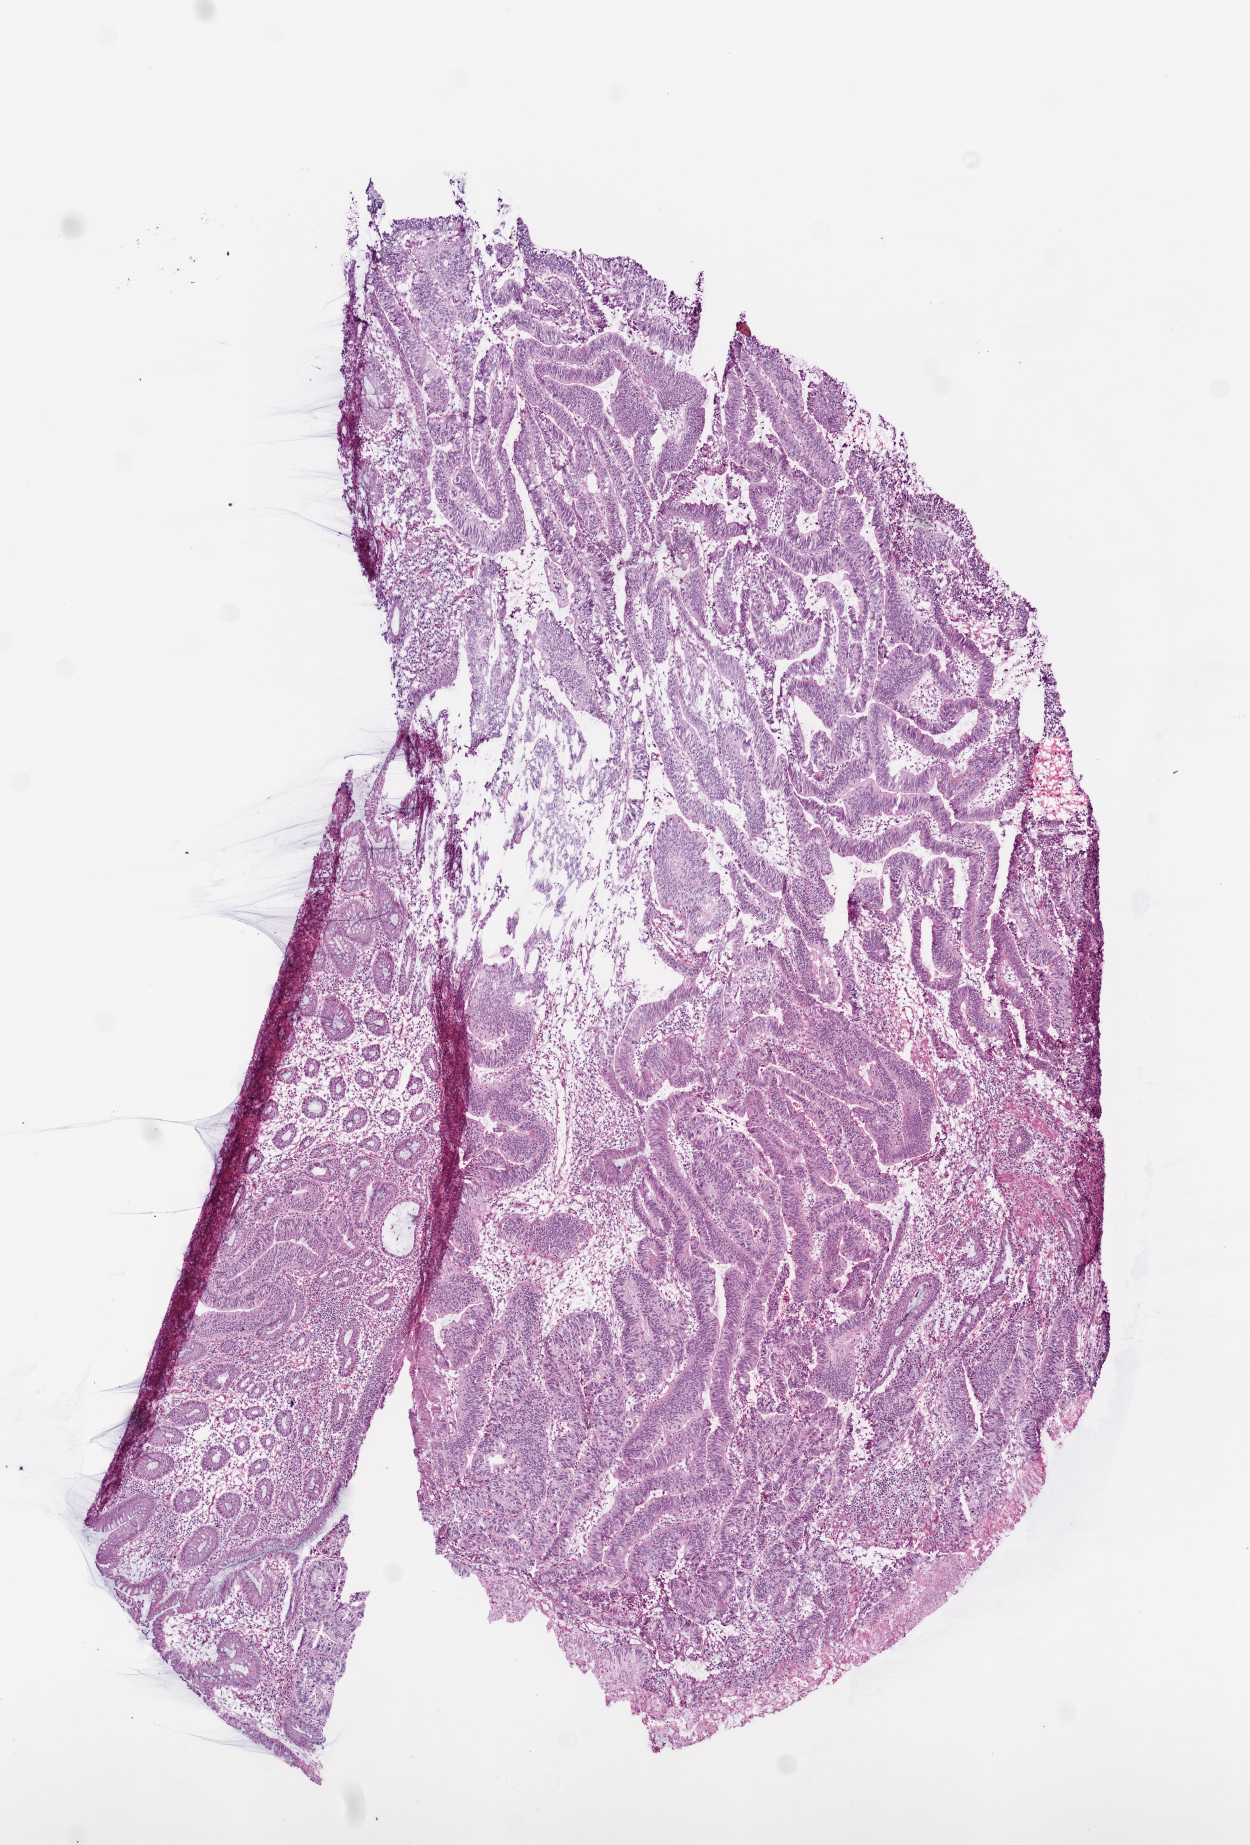
Whole-slide histology image, H&E-stained, shown as a low-resolution overview of the whole scanned area (about 5.0 x 7.4 mm). Frozen section from the top of the tissue portion. Sample: primary tumour, colon. Patient: male, age at initial diagnosis 72 years. Composition of this section per pathologist review: tumour cells 80%, tumour nuclei 80%, normal cells 8%, stromal cells 10%, necrosis 2%.
- histologic diagnosis: Adenocarcinoma, NOS
- AJCC pathologic stage: I (6th edition)